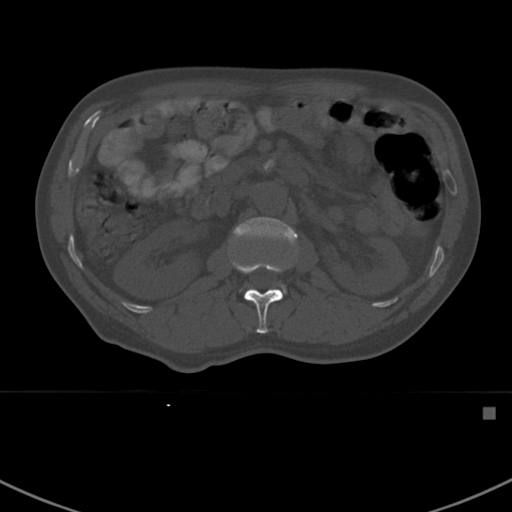
CT including the spine, one axial slice; slice 301 of 412 in the series (ordered by position); reconstruction kernel Br40s; 120 kVp; bone window (W 1800 / L 400 HU); 512 × 512 image matrix, field of view 358 × 358 mm. Patient: male, 59 years. From the clinical record (not read from this slice): primary cancer: prostate.
Structures marked on this image (semi-automatically segmented with operator editing):
- L1 vertebra: bounding box <231,261,291,334> (left, top, right, bottom; pixels)
- L2 vertebra: <231,216,298,293>